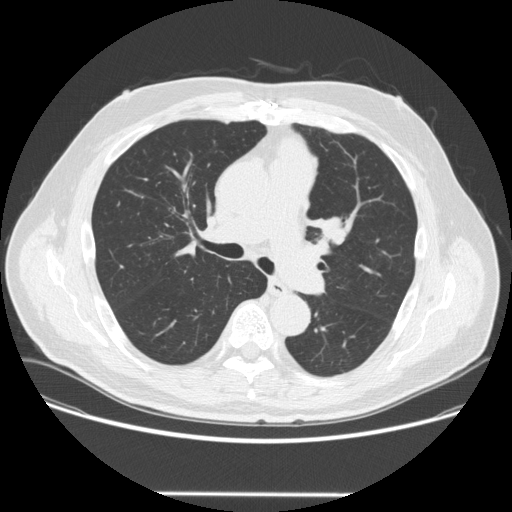
Chest CT (low-dose screening protocol), one axial image; third annual screen; lung window (W 1500 / L -600 HU); 120 kVp. Male, age 66 years at enrolment.
Lesion marked by an expert reader, bounding box (x1, y1, x2, y2) in pixels: (308, 205, 360, 254). The screening reader recorded 2 non-calcified nodules or masses ≥4 mm on this exam (left upper lobe, right lower lobe); which of them this box marks is not recorded. Official screen result: positive, other.